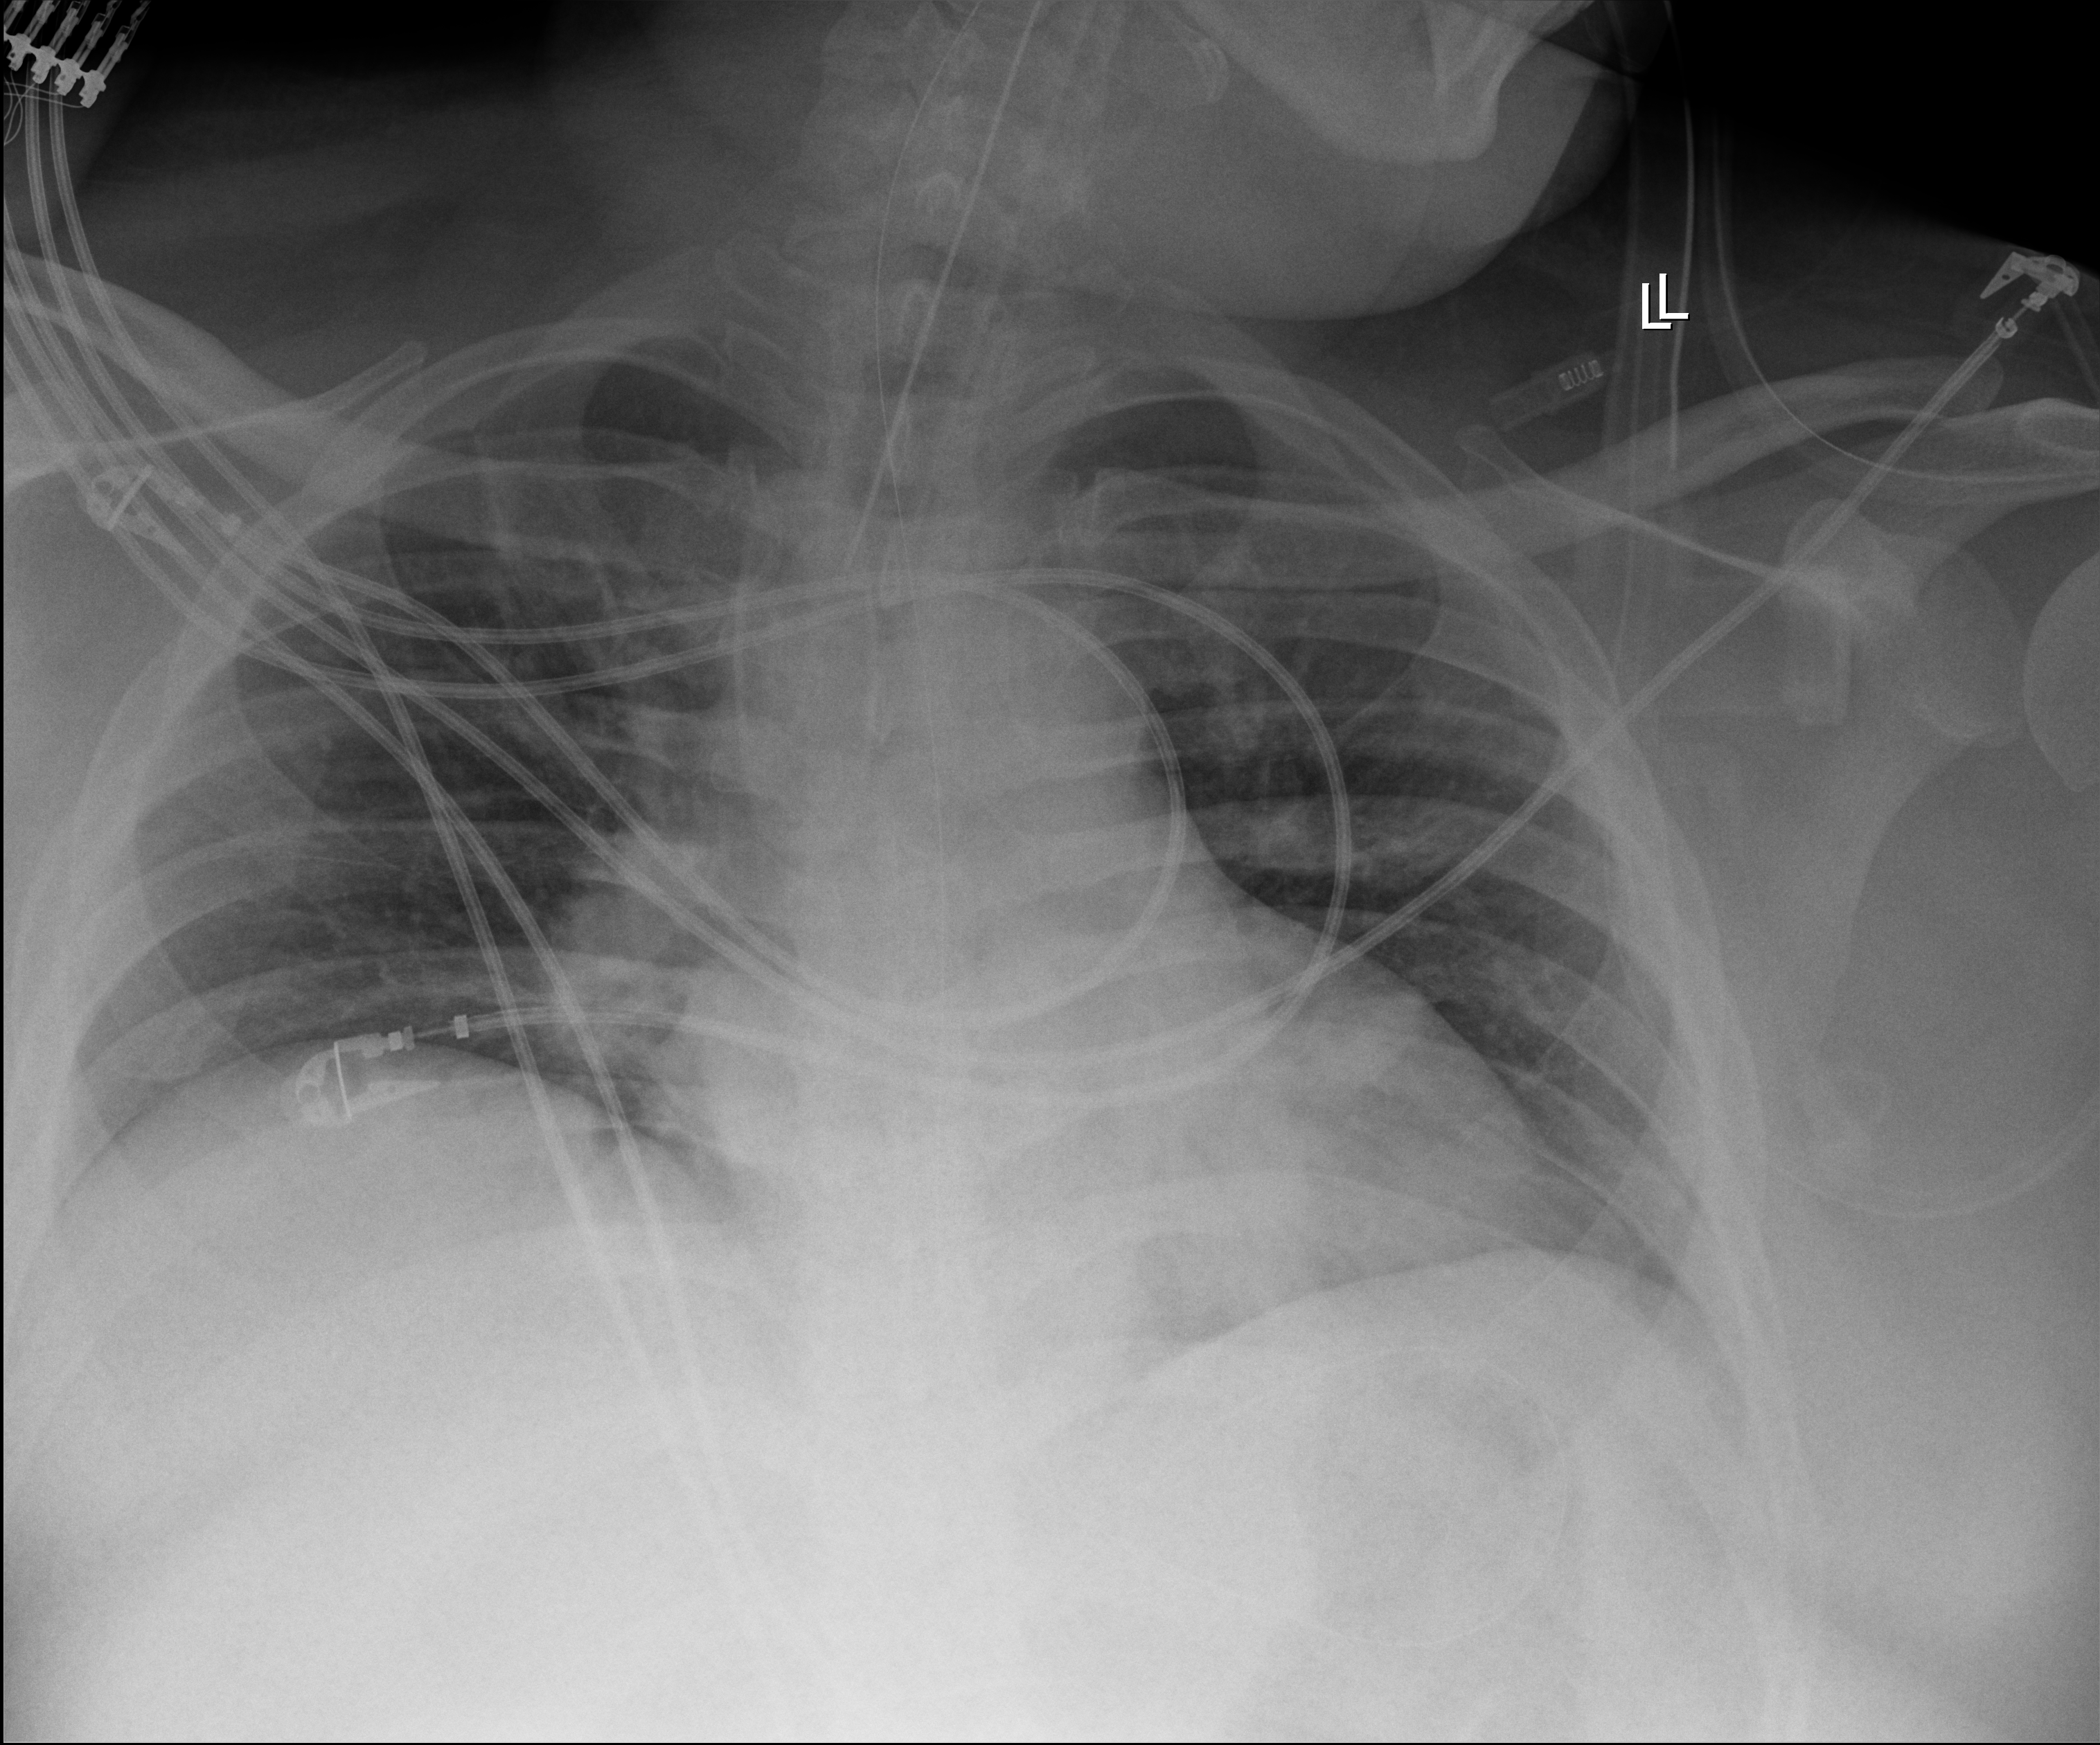
Chest X-ray (portable), anteroposterior (AP) projection. Male patient hospitalised with COVID-19, age 18–59 years.
Admission-level facts for this patient (not findings on this image; timing relative to this image not recorded): smoking status (admission record): never.